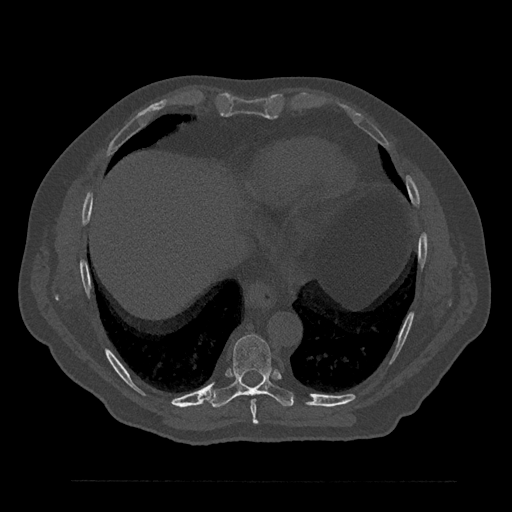
CT including the spine, one axial slice; position 415 of 797 along the scan axis; 120 kVp; bone window (W 1800 / L 400 HU); 0.5 mm slice thickness; 512 × 512 image matrix. Male patient, age 61 years. From the clinical record (not read from this slice): primary cancer: prostate.
Outlined on this slice (semi-automatically segmented with operator editing):
- T8 vertebra: bounding box <250,399,258,424> (left, top, right, bottom; pixels)
- T9 vertebra: <208,335,295,408>